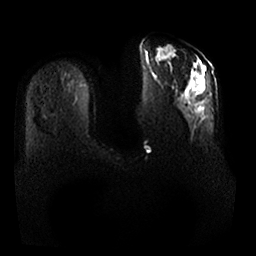
Breast MRI, one axial slice. Position 7 of 25 along the scan axis. Diffusion-weighted series; image 2 of 4 stored at this slice position (different b-values; order by instance number). 1.5 T. 256 × 256 image matrix, field of view 380 × 380 mm. Female patient.
Outlined on this slice (outlined manually by an expert reader):
- tumour on diffusion-weighted imaging: bounding box <159,49,205,89> (left, top, right, bottom; pixels)